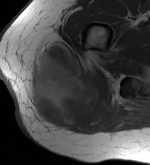
MRI of an extremity soft-tissue mass, one axial slice; position 19 of 56 along the scan axis; MR volume resampled by the dataset authors to the PET/CT grid (not the native acquisition matrix); 3.27 mm slice thickness; 150 × 165 image matrix, field of view 146 × 161 mm. Female patient. Case-level facts recorded for this patient, not image findings: histological type: epithelioid sarcoma with vascular differentiation; site of the primary tumour: right buttock.
Annotated regions visible in this slice (expert contour drawn on MRI and transferred to this co-registered scan by the dataset authors):
- gross tumour volume (mass): bounding box <25,40,111,130> (left, top, right, bottom; pixels)